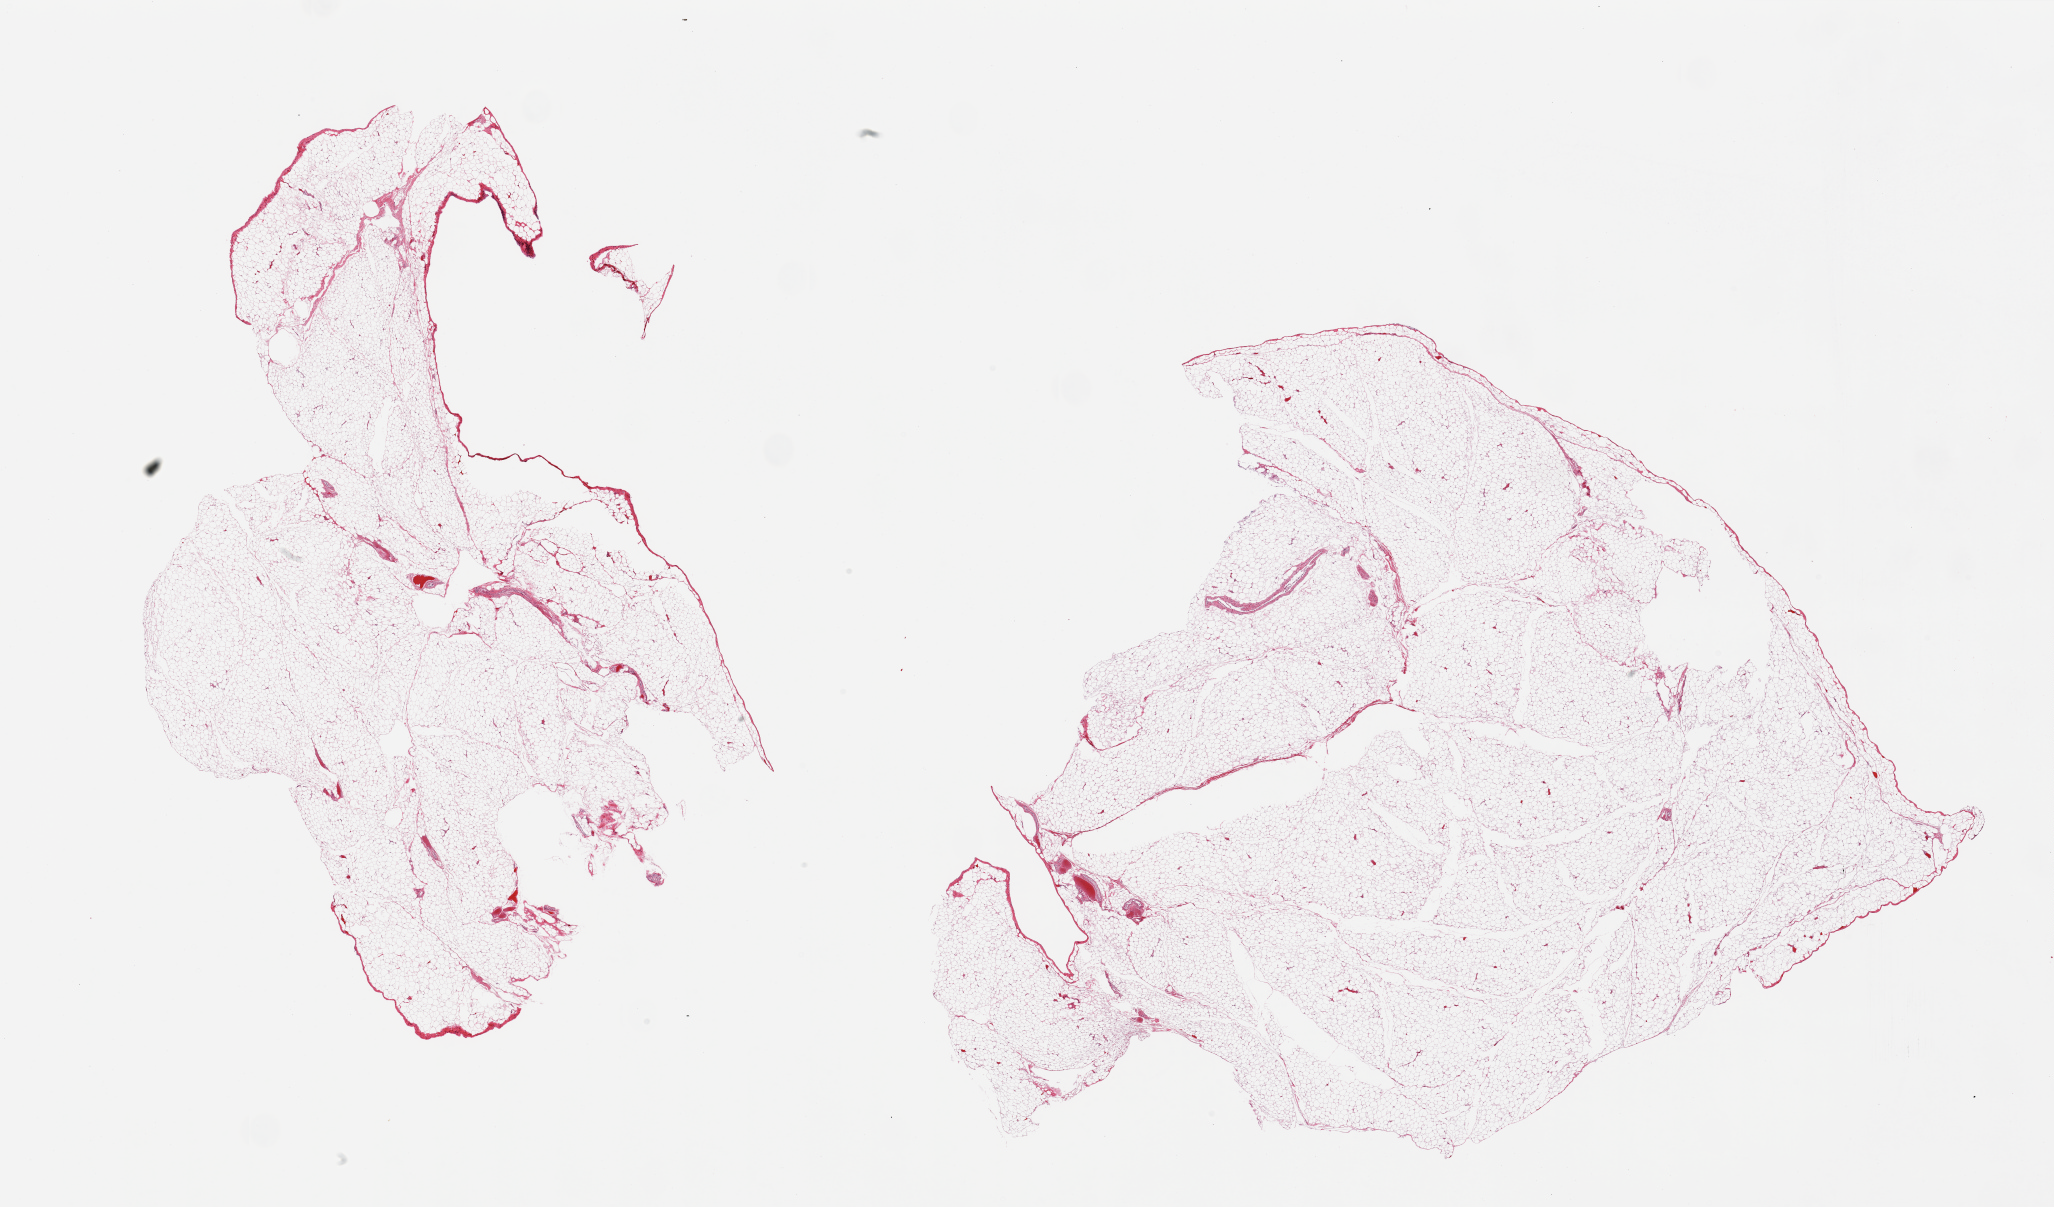
Digitized H&E-stained section, low-resolution overview of the scanned area, about 32.5 x 19.1 mm. PAXgene-fixed paraffin-embedded (PFPE) section. Sampled site (target tissue): omentum. Donor tissue sample. Donor sex: female.
Review note (as recorded): 2 pieces, minimal interstital fascia/vascular elements.